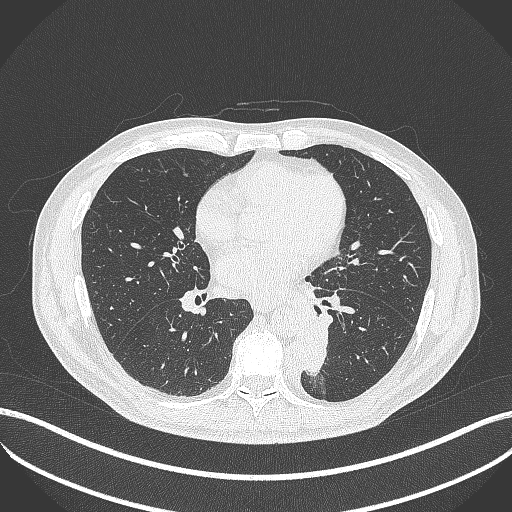
Chest CT, one axial slice. Slice 190 of 451 in the series (ordered by position). Reconstruction kernel B70f. Lung window (W 1500 / L -600 HU). 512 × 512 image matrix, field of view 400 × 400 mm. Male patient, age 72 years. From the clinical record (not read from this slice): clinical TNM (as recorded): T2b N0 M1.
Outlined on this slice (bounding box drawn by a radiologist):
- lung tumour (recorded histology: adenocarcinoma): box from (x=296, y=323) to (x=332, y=377) px